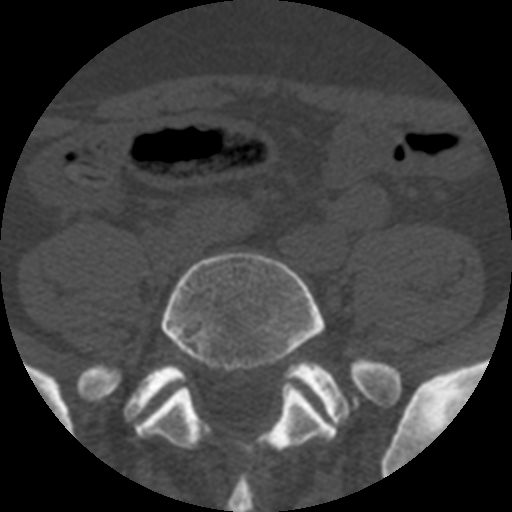
CT including the spine, one axial slice; position 58 of 508 along the scan axis; reconstruction kernel STANDARD; 120 kVp; bone window (W 1800 / L 400 HU); 1.25 mm slice thickness; 512 × 512 image matrix. Patient age 57 years. Case-level facts recorded for this patient, not image findings: primary cancer: prostate.
Annotated regions visible in this slice (semi-automatically segmented with operator editing):
- L5 vertebra: bounding box (x1, y1, x2, y2) in pixels: (135, 252, 391, 454)